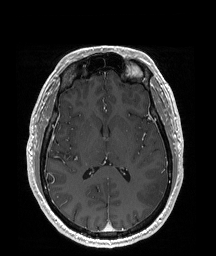
Brain MRI from a brain-tumour surgery series, one axial slice; slice 95 of 192 in the series (ordered by position); T1-weighted post-contrast; 216 × 256 image matrix, field of view 219 × 260 mm. Case-level facts recorded for this patient, not image findings: histopathology: Glioblastoma; WHO grade: 4.
Outlined on this slice (outlined manually by an expert reader):
- tumour: bounding box <137,172,168,210> (left, top, right, bottom; pixels)